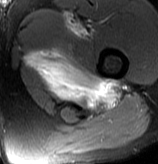
MRI of an extremity soft-tissue mass, one axial slice; slice 67 of 70 in the series (ordered by position); T2-weighted fat-saturated; MR volume resampled by the dataset authors to the PET/CT grid (not the native acquisition matrix); 3.27 mm slice thickness; 158 × 164 image matrix. Male patient. From the clinical record (not read from this slice): histological type: extraskeletal osteosarcoma; grade: high; site of the primary tumour: left adductur.
Structures marked on this image (expert contour drawn on MRI and transferred to this co-registered scan by the dataset authors):
- gross tumour volume (mass): bounding box [x1, y1, x2, y2] px = [24, 12, 126, 111]